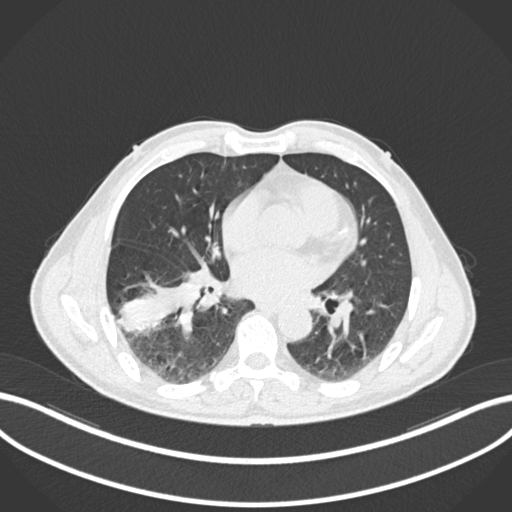
Chest CT, one axial slice; slice 87 of 208 in the series (ordered by position); reconstruction kernel B30f; 120 kVp; lung window (W 1500 / L -600 HU); 1 mm slice thickness; 512 × 512 image matrix, field of view 400 × 400 mm. Patient: male, 58 years. From the clinical record (not read from this slice): clinical TNM (as recorded): T3 N0 M0.
Structures marked on this image (rectangle marked by the reading radiologist):
- lung tumour (recorded histology: squamous cell carcinoma): bounding box <117,273,200,334> (left, top, right, bottom; pixels)